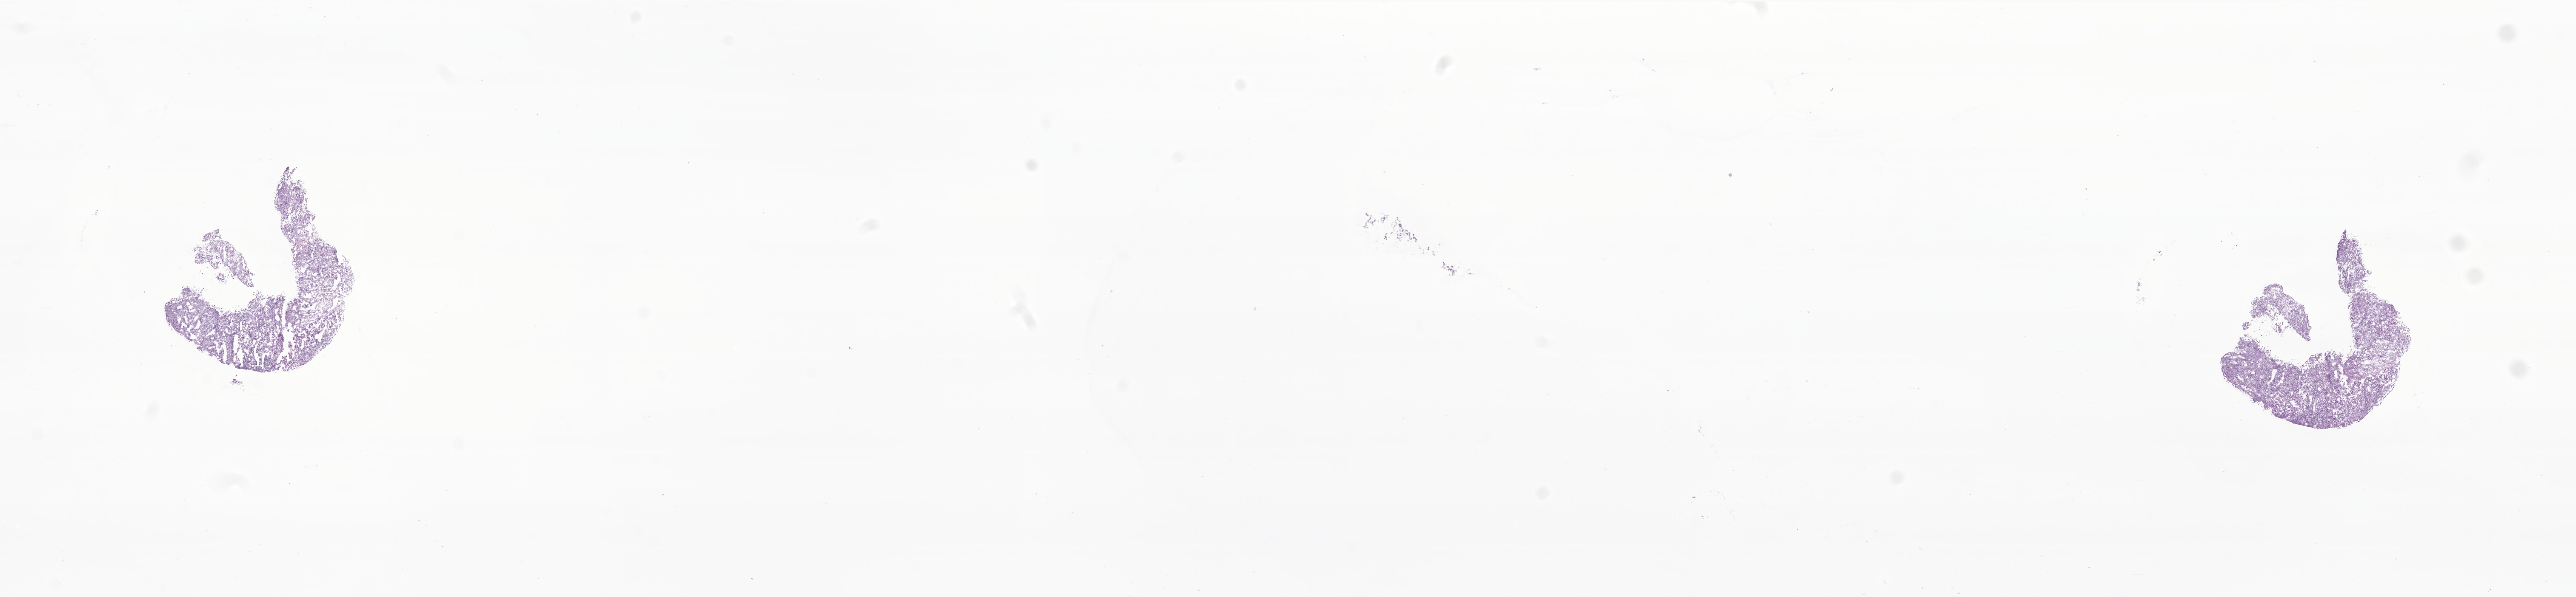
Haematoxylin and eosin whole-slide image of tumor tissue from the lower limb lymph node, a low-resolution overview of the entire scanned area, about 28.8 x 6.7 mm; frozen section (OCT-embedded). Patient: male, age 146 months (12 years 2 months).
Recorded diagnosis: Carcinoma, metastatic, NOS.